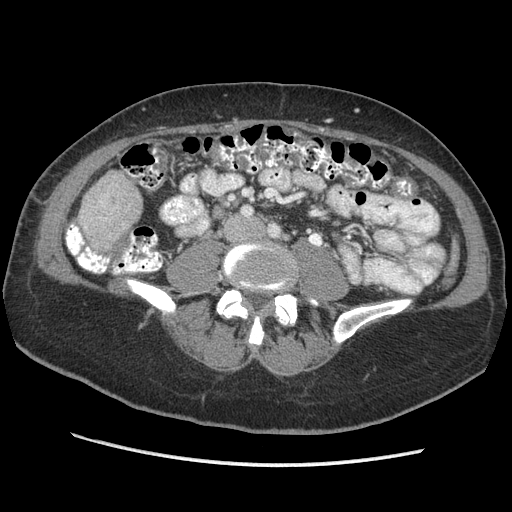
Contrast-enhanced abdominal CT (liver protocol), one axial slice; 140 kVp; soft-tissue window (W 400 / L 40 HU); 2.5 mm slice thickness; 512 × 512 image matrix, field of view 360 × 360 mm. Case-level facts recorded for this patient, not image findings: diagnosis: hepatocellular carcinoma (patient treated with transarterial chemoembolisation; whether this scan precedes or follows treatment is not stated here); TNM stage (as recorded): Stage-II; Child-Pugh class: A; tumour differentiation: no biopsy.
Outlined on this slice (semi-automatic segmentation, software-assisted and operator-edited):
- liver parenchyma outside the tumour (the mass and vessels are separate outlines, so this box may not span the whole liver): box from (x=78, y=172) to (x=142, y=248) px